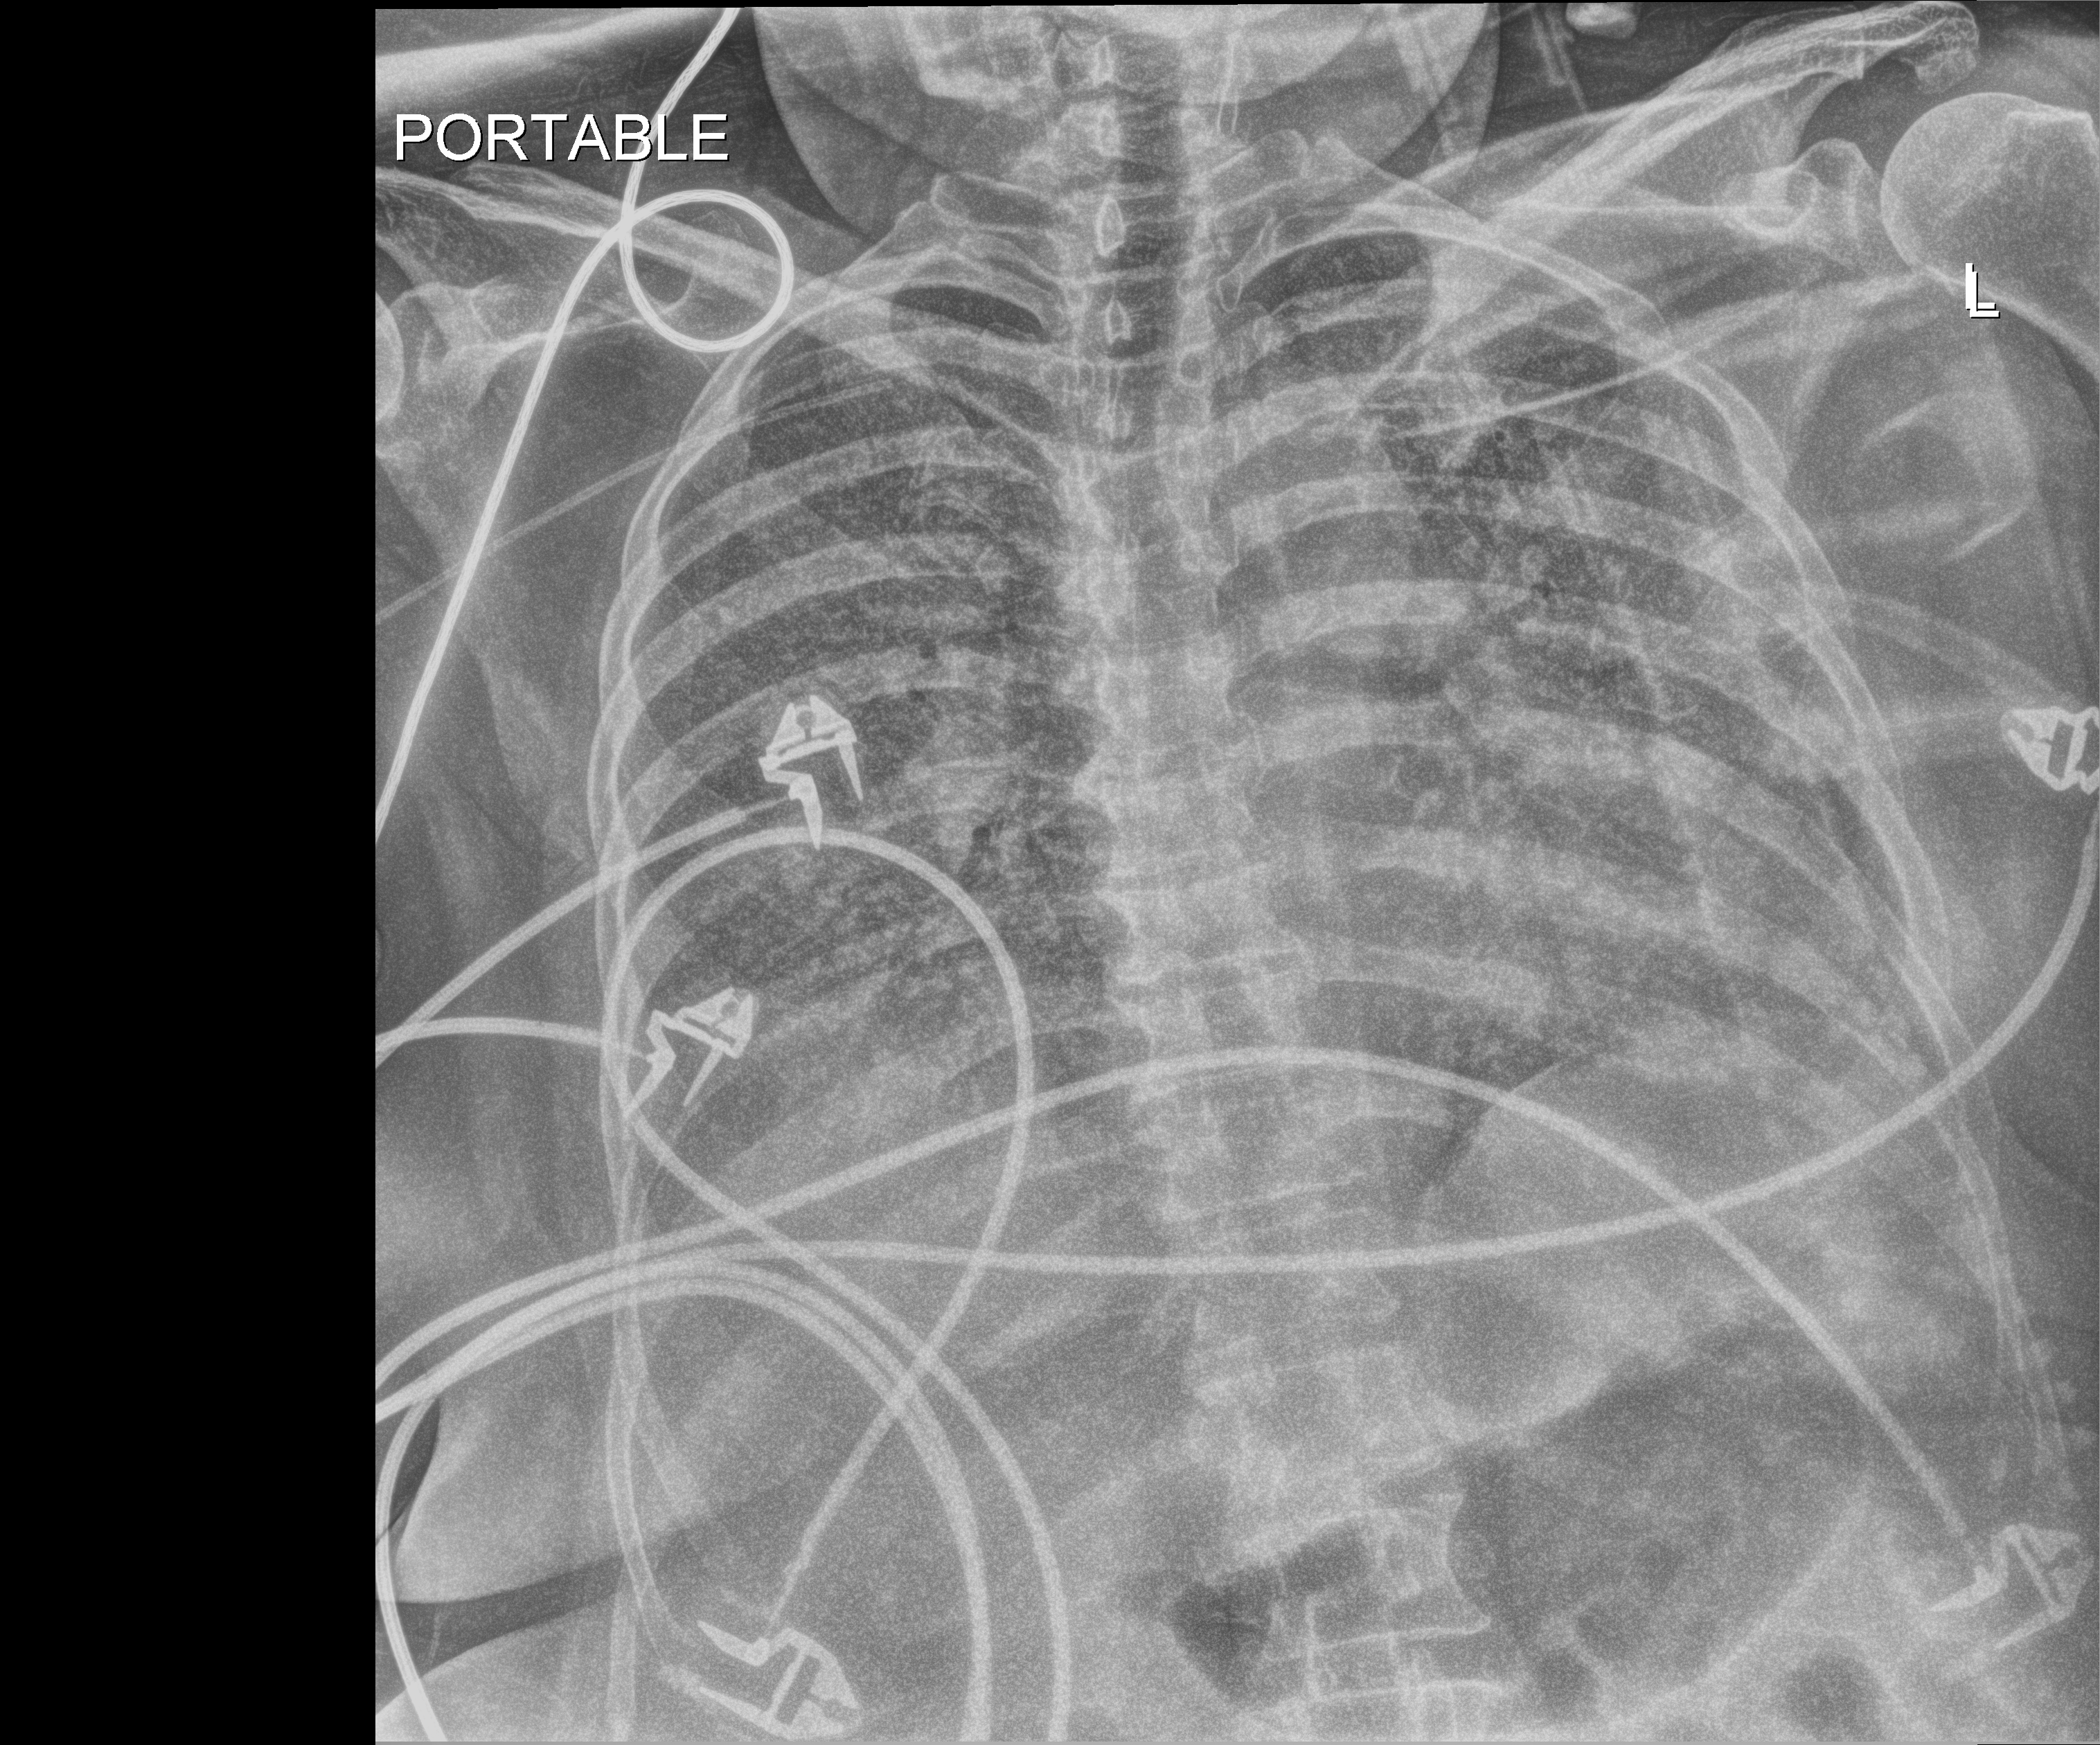
Chest X-ray. Female patient hospitalised with COVID-19, age 60–74 years.
From the hospital-stay record, not from the radiograph (when in the stay this image was taken is not recorded):
- diabetes (admission record): no